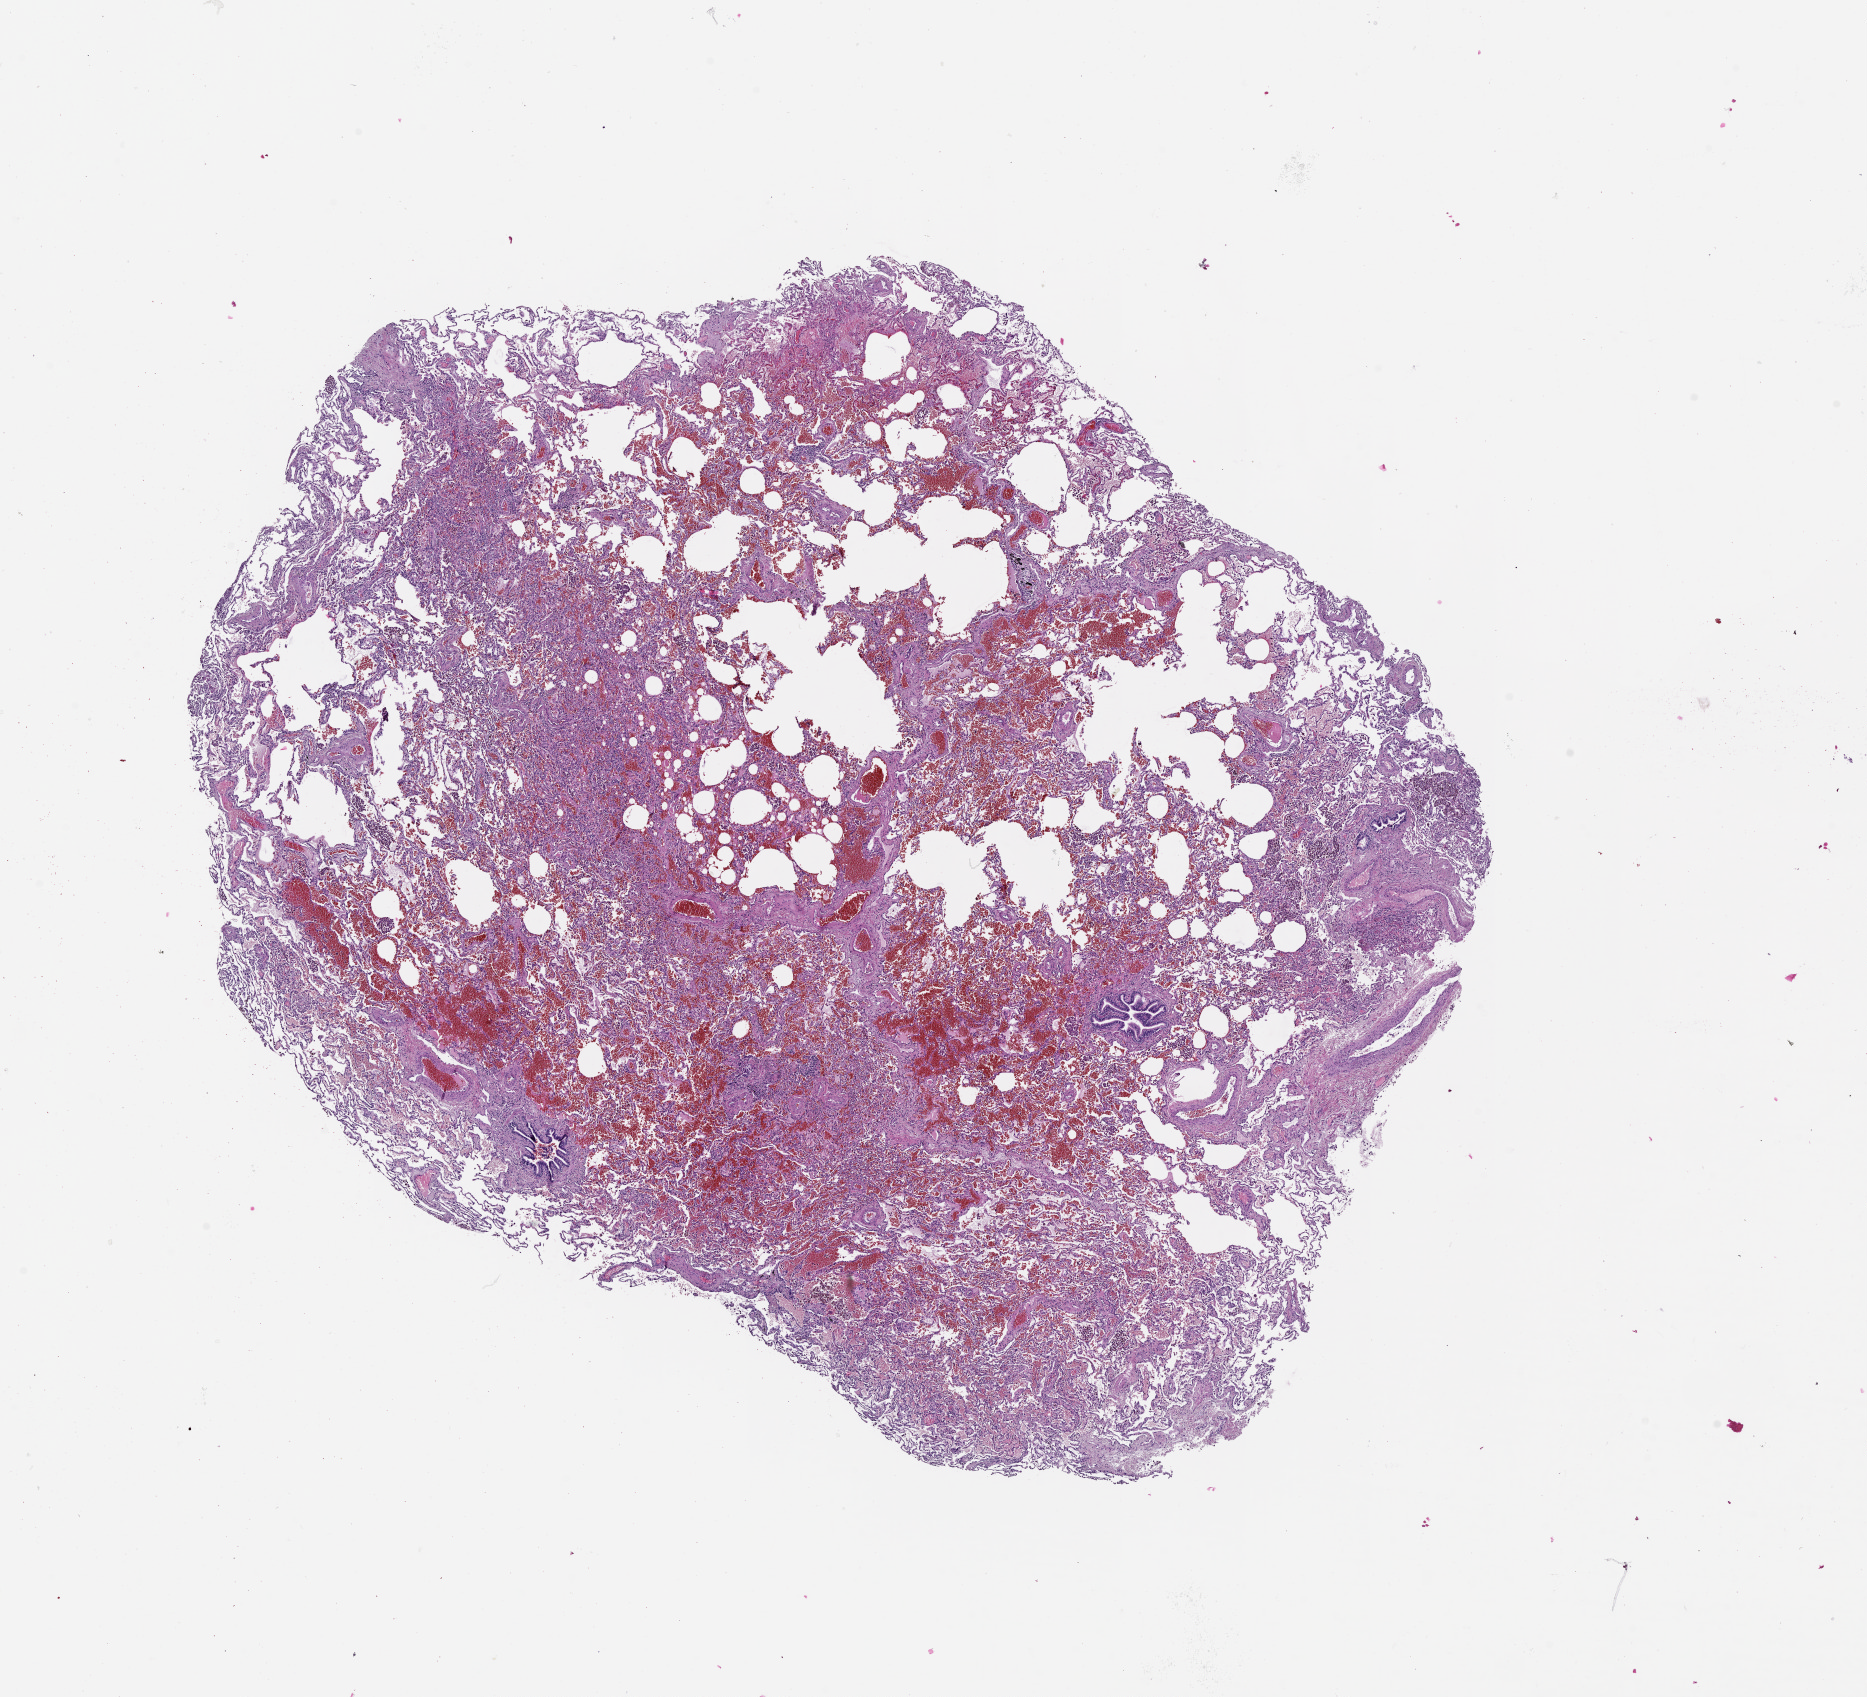
Whole-slide histology image, H&E, whole scanned area (about 15.0 x 13.7 mm, slide scanned at 20x) shown as a low-resolution overview. Lung, normal (non-tumour) tissue. Patient: male, age 55 years.
• this section: normal (non-tumour) tissue from the same patient
• patient diagnosis (cohort enrolment): squamous cell carcinoma (lung)